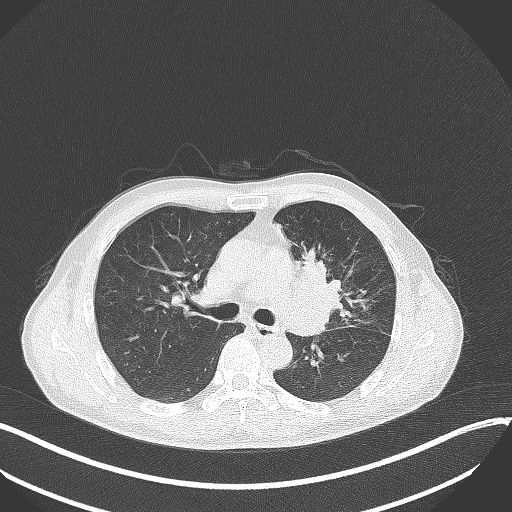
Chest CT, one axial slice; slice 209 of 411 in the series (ordered by position); 120 kVp; lung window (W 1500 / L -600 HU); 512 × 512 image matrix. Patient: male, 56 years. From the clinical record (not read from this slice): clinical TNM (as recorded): T2a N0 M0.
Outlined on this slice (bounding box drawn by a radiologist):
- lung tumour (recorded histology: squamous cell carcinoma): bounding box (x1, y1, x2, y2) in pixels: (290, 244, 350, 324)